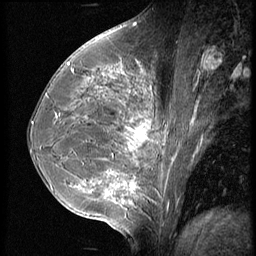
Breast MRI (dynamic contrast-enhanced), one sagittal slice. Slice 27 of 56 in the series (ordered by position). 3 images stored at this slice position (order not interpretable as contrast timing). 1.5 T. TE 4.2 ms, TR 9 ms. 2.5 mm slice thickness. 256 × 256 image matrix, field of view 180 × 180 mm. Female patient, age 35 years. Case-level facts recorded for this patient, not image findings: setting: breast cancer imaged before/during neoadjuvant chemotherapy; receptor status: HR-positive, HER2-negative.
Outlined on this slice (semi-automatically segmented with operator editing):
- analysis volume of interest (the breast-tissue region the enhancement analysis was run in; not a lesion): box from (x=63, y=60) to (x=186, y=218) px
- tumour enhancement mask (voxels above the 140 % enhancement threshold inside the analysis volume of interest): (x=68, y=64)–(x=153, y=204)